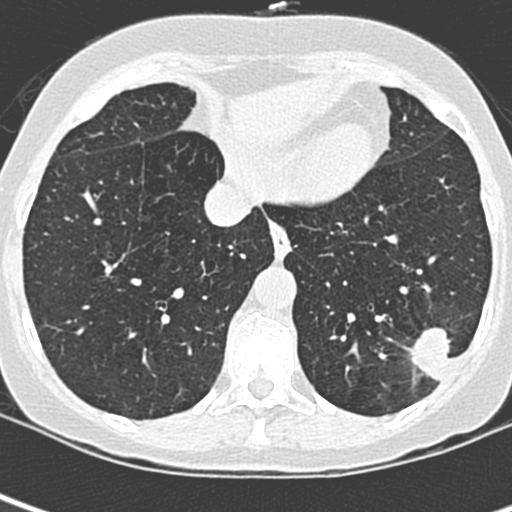
Low-dose screening chest CT, one axial slice; slice 84 of 252 in the series (ordered by position); lung window (W 1500 / L -600 HU); 512 × 512 image matrix, field of view 271 × 271 mm.
Structures marked on this image (expert manual segmentation):
- lesion 1 (tumor, lower lobe of left lung): bounding box (x1, y1, x2, y2) in pixels: (411, 327, 456, 382)